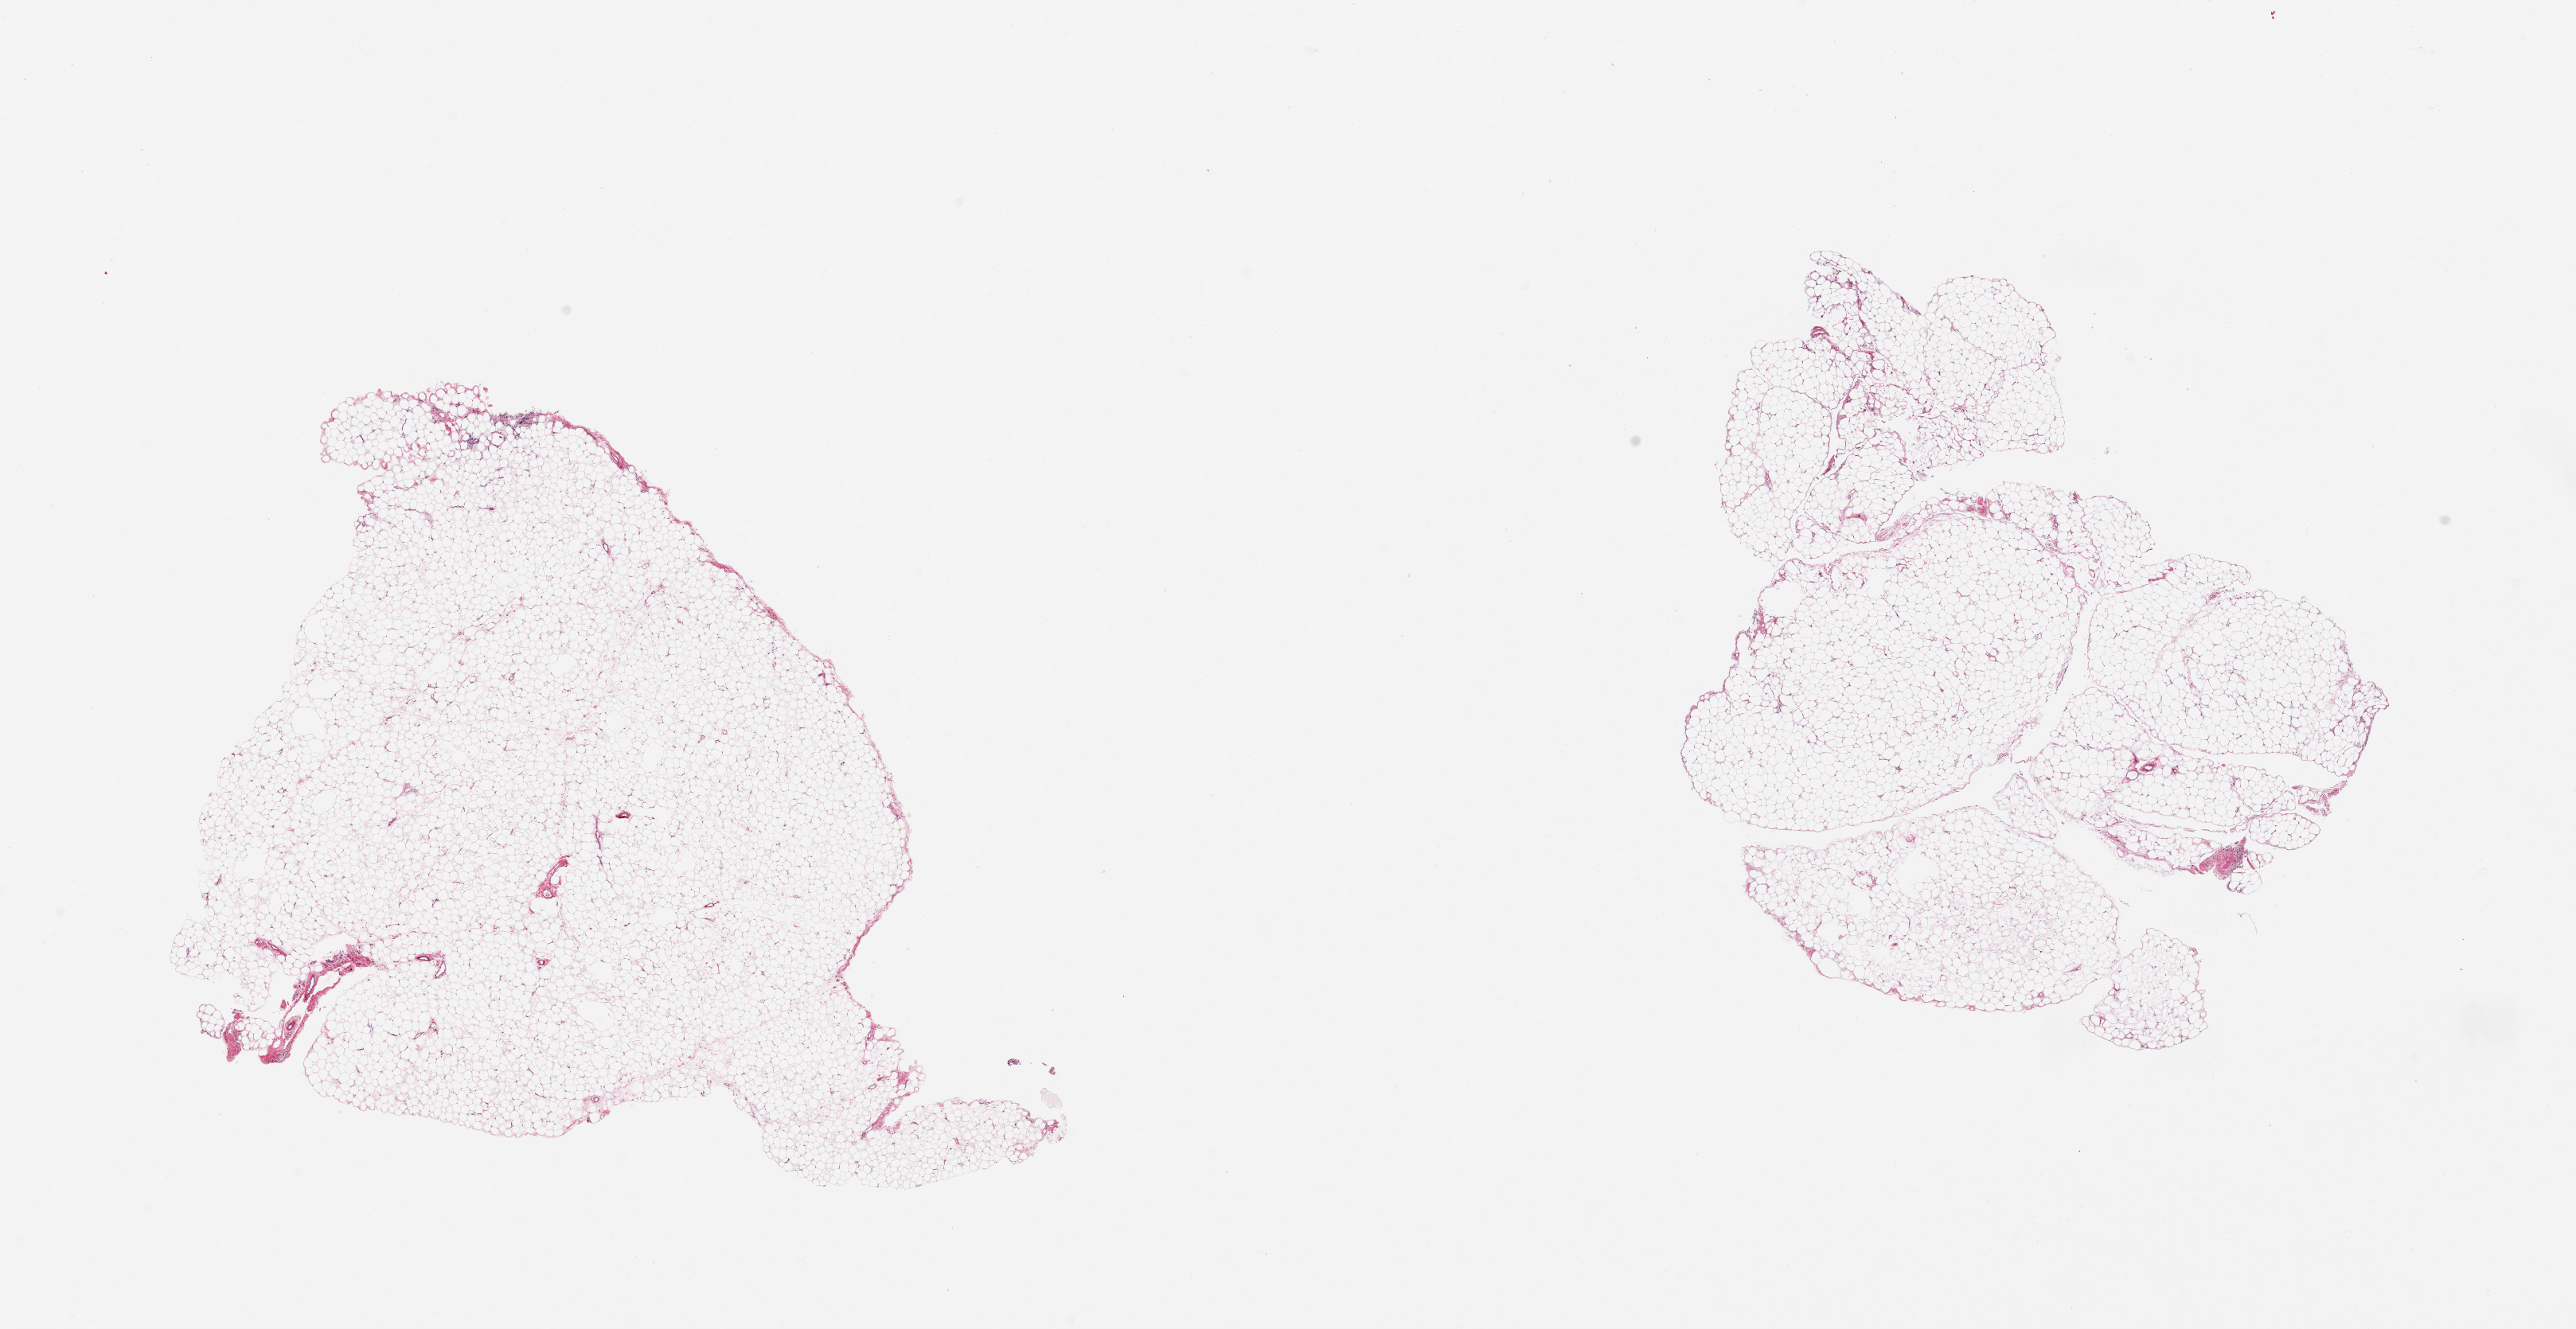
Whole-slide image, hematoxylin and eosin (H&E) stain — a low-resolution overview of the entire scanned area, about 25.6 x 13.2 mm. PAXgene-fixed, paraffin-embedded tissue. Sampled site (target tissue): omentum. Donor tissue sample. Female donor.
Review note (as recorded): 2 pieces.